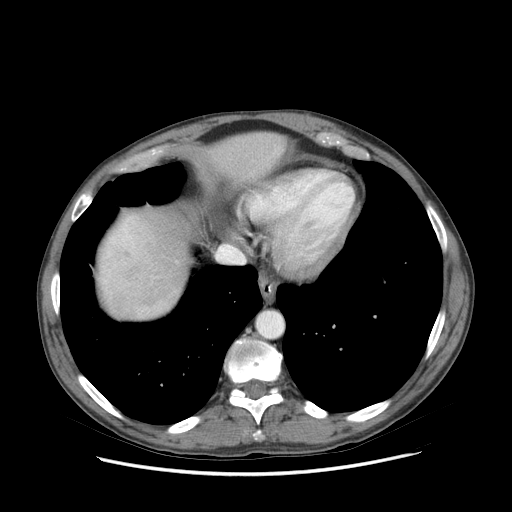
Contrast-enhanced abdominal CT (liver protocol), one axial slice. Position 73 of 89 along the scan axis. Soft-tissue window (W 400 / L 40 HU). 512 × 512 image matrix. From the clinical record (not read from this slice): diagnosis: hepatocellular carcinoma (patient treated with transarterial chemoembolisation; whether this scan precedes or follows treatment is not stated here); TNM stage (as recorded): Stage-IIIB.
Structures marked on this image (semi-automatic segmentation, software-assisted and operator-edited):
- abdominal aorta: box from (x=258, y=312) to (x=282, y=337) px
- liver parenchyma outside the tumour (the mass and vessels are separate outlines, so this box may not span the whole liver): (x=98, y=132)–(x=284, y=318)
- liver vessels: (x=104, y=218)–(x=135, y=283)